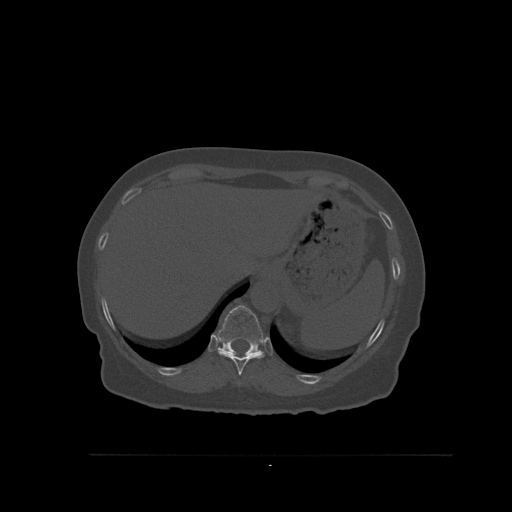
CT including the spine, one axial slice. Slice 312 of 527 in the series (ordered by position). Bone window (W 1800 / L 400 HU). 1.5 mm slice thickness. 512 × 512 image matrix, field of view 470 × 470 mm. Female patient, age 73 years. Case-level facts recorded for this patient, not image findings: primary cancer: breast; vertebrae with lytic lesions (as recorded): L2.
Annotated regions visible in this slice (semi-automatic segmentation, software-assisted and operator-edited):
- T10 vertebra: bounding box <217,347,265,376> (left, top, right, bottom; pixels)
- T11 vertebra: <218,305,264,355>